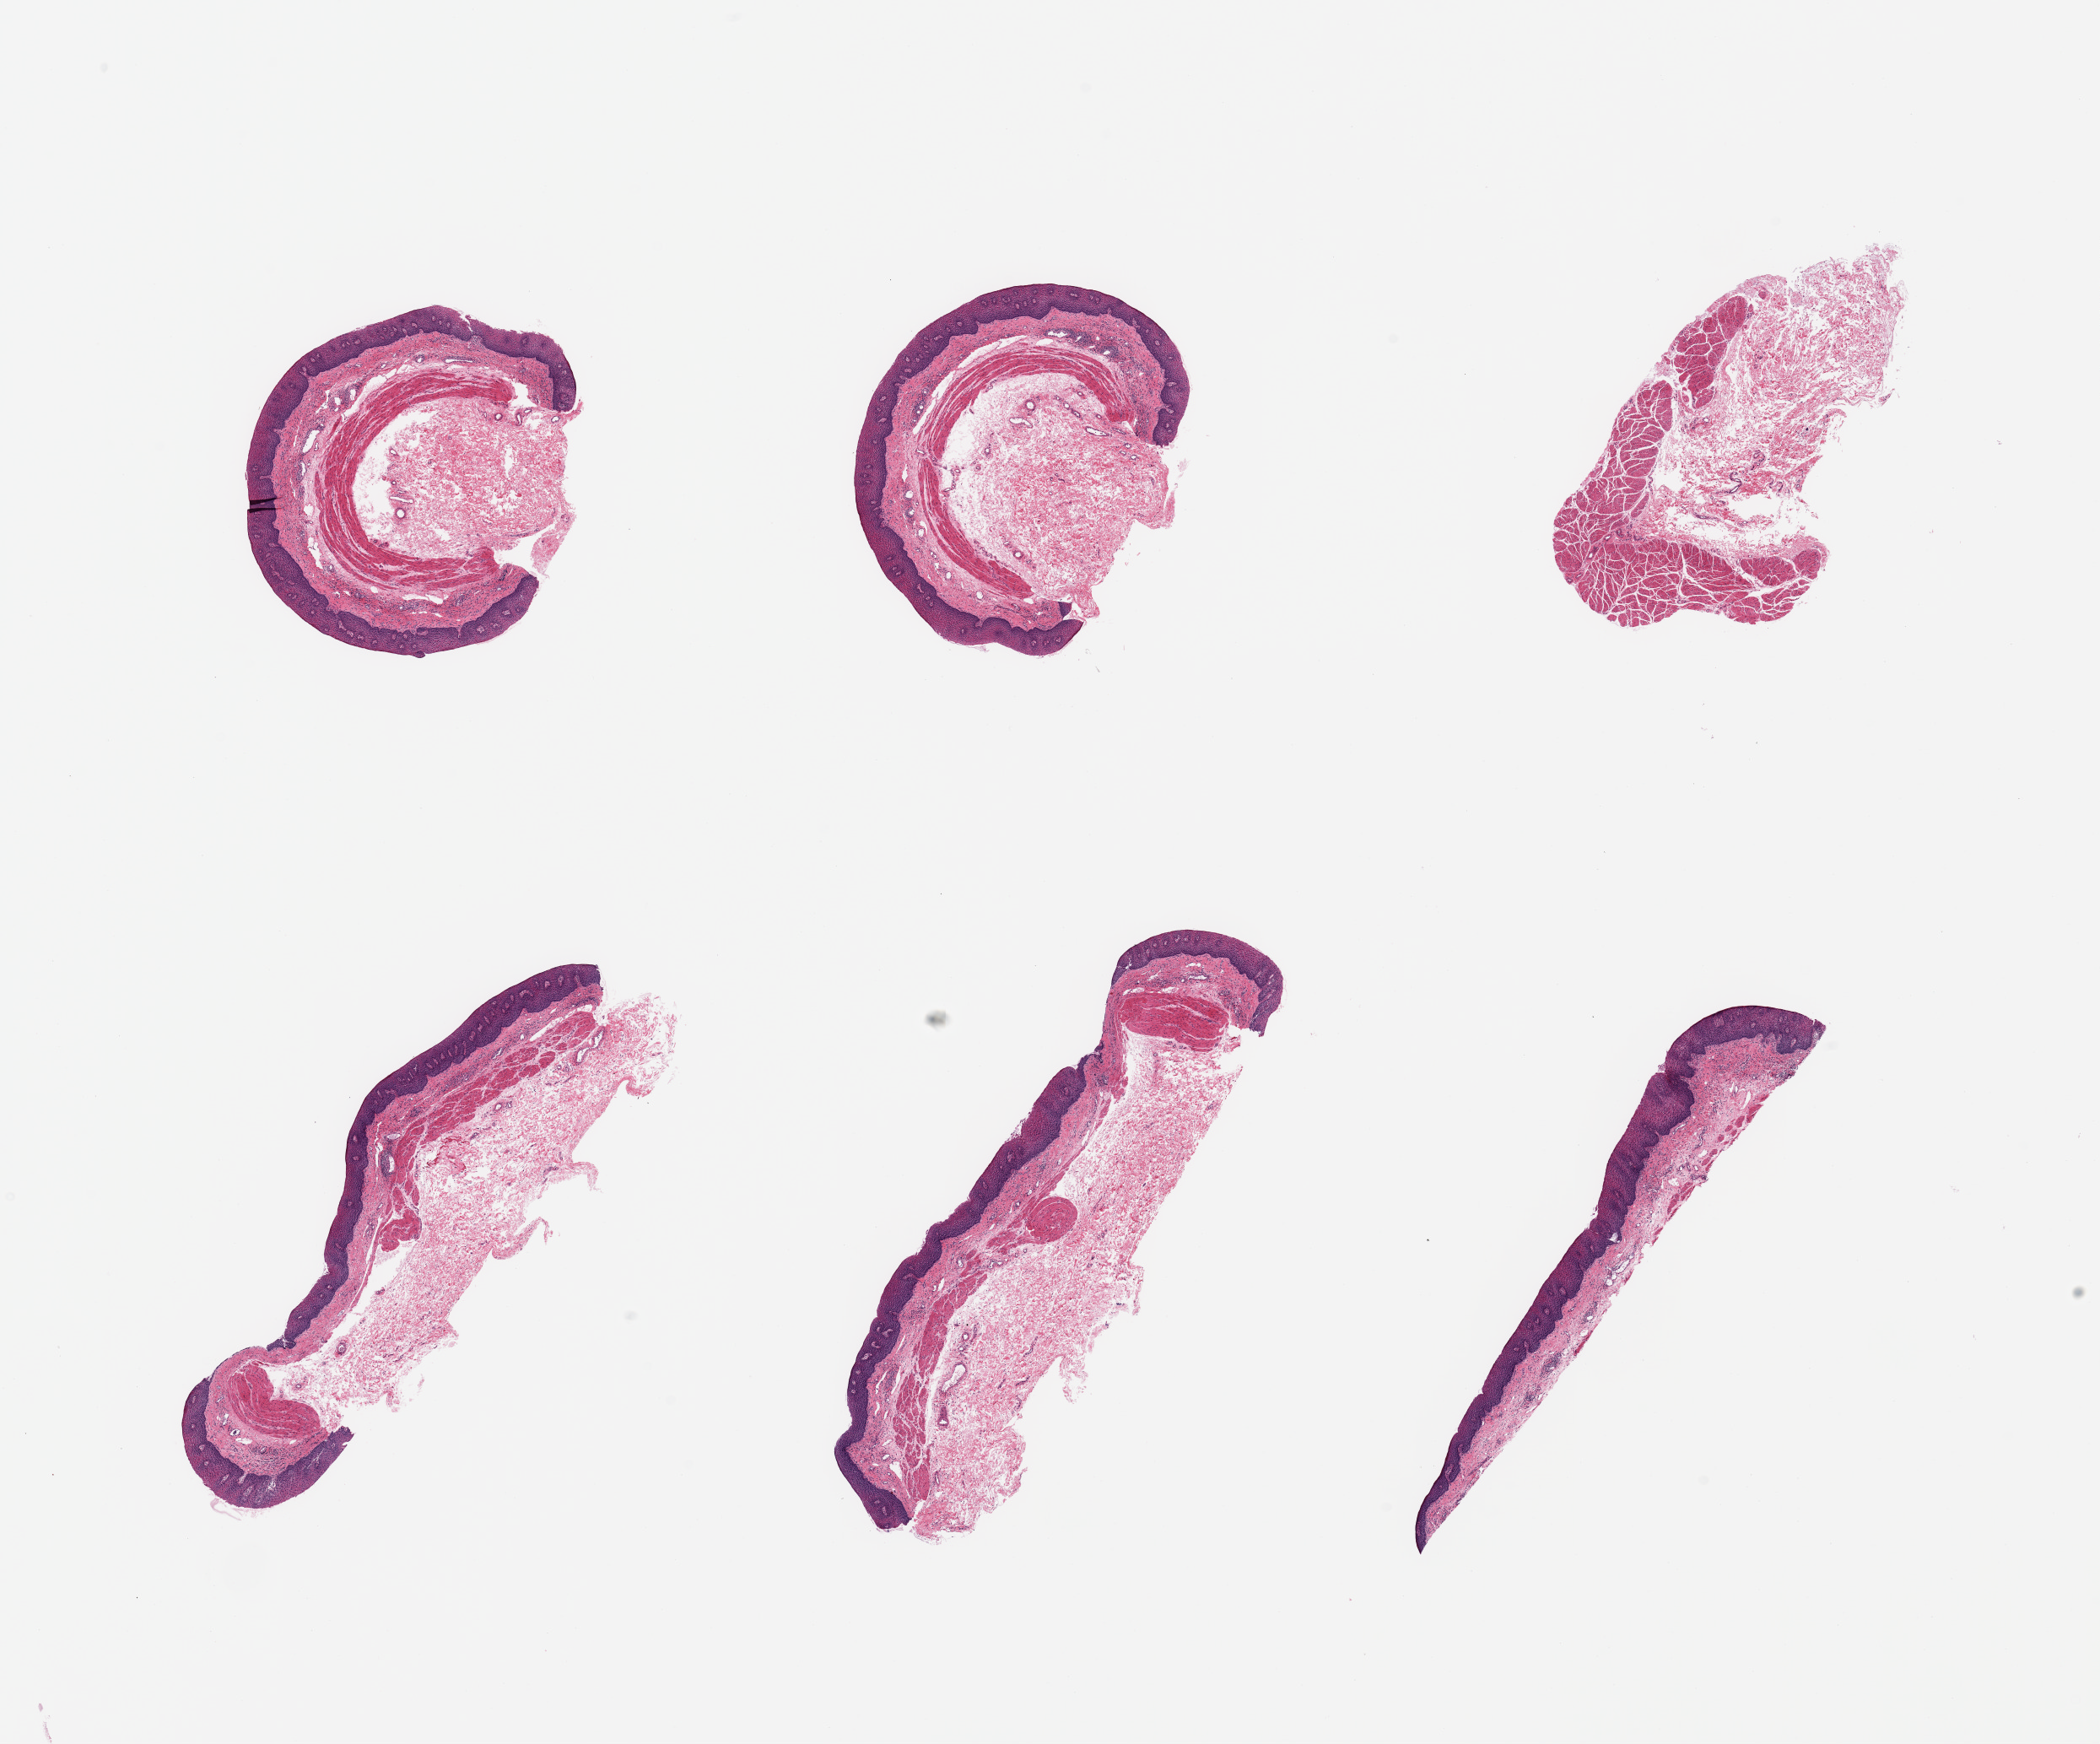
Digitized H&E-stained section, brightfield, shown as a low-resolution overview of the whole scanned area (about 19.7 x 16.4 mm, from a 20x scan), PAXgene-fixed, paraffin-embedded tissue, sampled site (target tissue): esophageal mucous membrane, donor tissue sample. Donor sex: female.
Reviewer comment on this tissue sample: 6 pieces, squamous mucosa up to ~0.25mm, ~15-20% thickness.